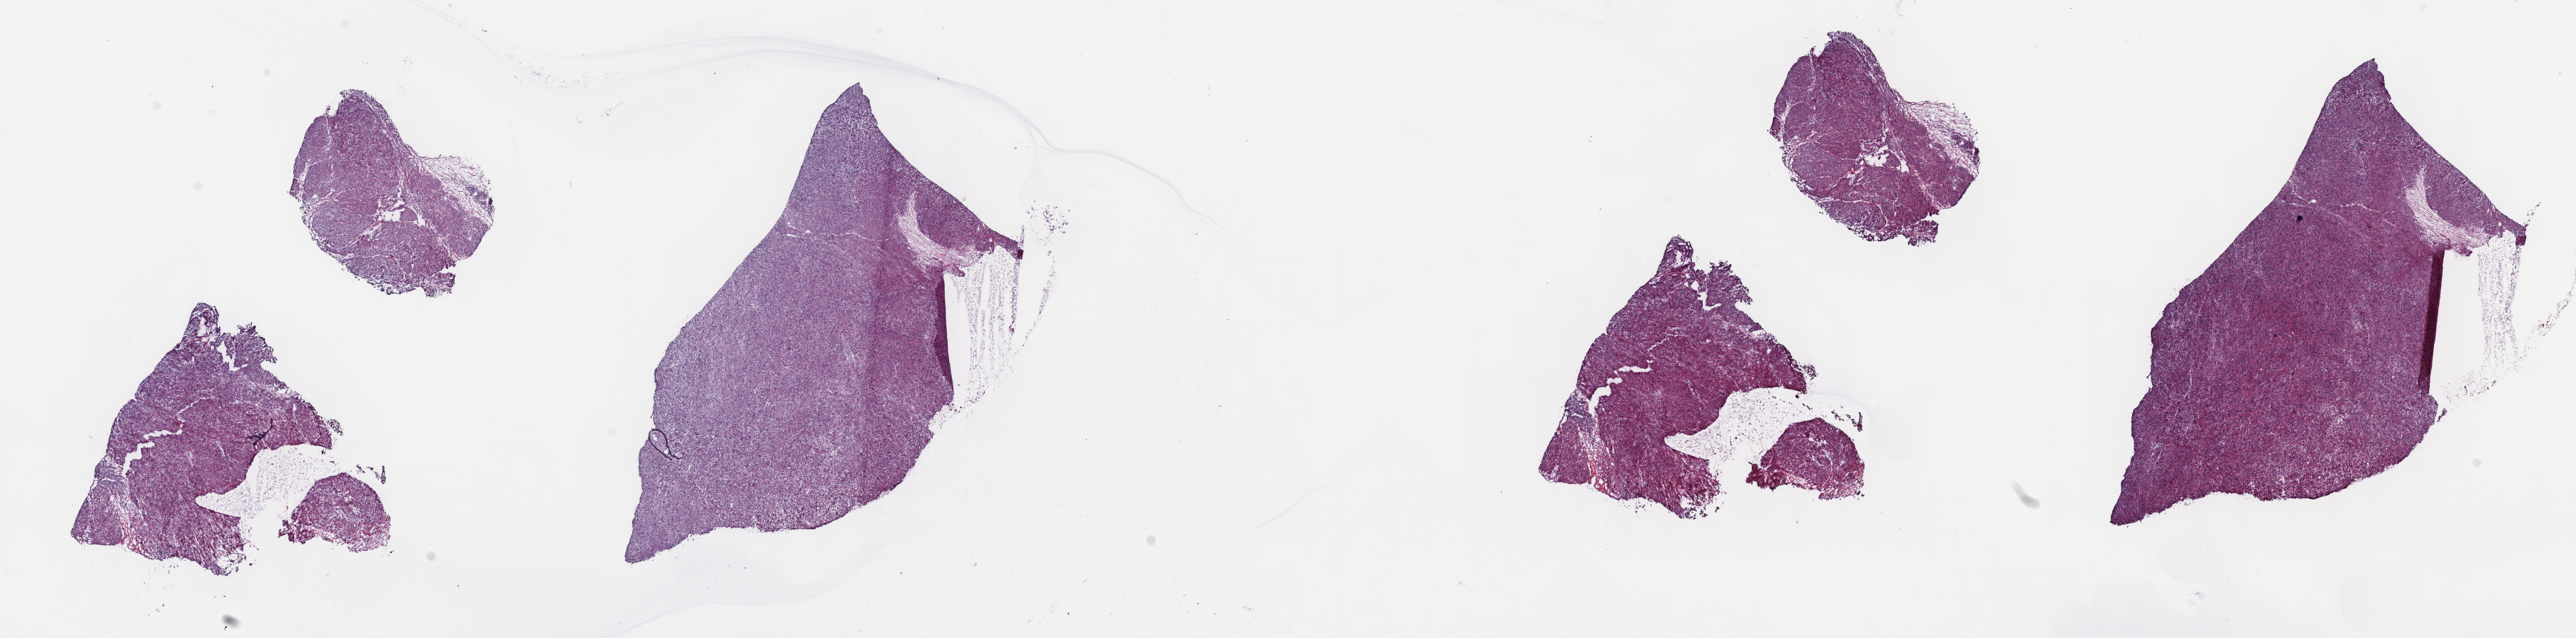
Digitized Hematoxylin and eosin (H&E) stained tissue section (whole slide) — shown as a low-resolution overview of the whole scanned area (about 29.2 x 7.2 mm); frozen section from the top of the tissue portion; sample: primary tumour, retroperitoneum and peritoneum. Female patient; age at initial diagnosis 66 years. Slide review estimates, as recorded: tumour cells 100%, tumour nuclei 80%, normal cells 0%, stromal cells 0%, necrosis 0%. Infiltration values recorded for this section: lymphocyte infiltration 1%, monocyte infiltration 0%, neutrophil infiltration 0%.
Pathologic diagnosis: Leiomyosarcoma, NOS.